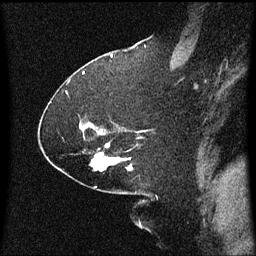
Breast MRI (dynamic contrast-enhanced), one sagittal slice. Slice 36 of 60 in the series (ordered by position). Dynamic contrast-enhanced series, image 2 of 3 at this slice position (ordered by acquisition). 1.5 T. TE 4.2 ms, TR 8 ms. 2.1 mm slice thickness. 256 × 256 image matrix, field of view 200 × 200 mm. Female patient, age 59 years.
Annotated regions visible in this slice (semi-automatic segmentation, software-assisted and operator-edited):
- analysis volume of interest (the breast-tissue region the enhancement analysis was run in; not a lesion): bounding box <90,144,133,171> (left, top, right, bottom; pixels)
- tumour enhancement mask (voxels above the 70 % enhancement threshold inside the analysis volume of interest): <90,154,131,171>